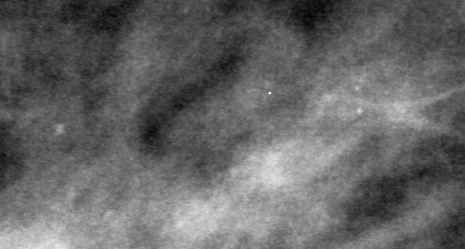
Region of interest cut from a scanned film mammogram (one marked finding); left breast; MLO view.
- Marked abnormality: calcifications, morphology punctate, distribution linear; BI-RADS assessment category 4; subtlety rating 1 on a 1 (subtle) to 5 (obvious) scale; pathology result (as recorded, not read from the image): benign.